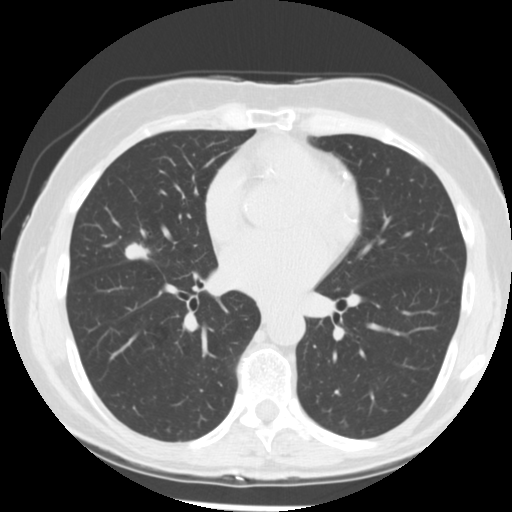
Chest CT (low-dose screening protocol), one axial image. First (baseline) screen. Lung window (W 1500 / L -600 HU). 2.5 mm slice thickness. Standard (soft-tissue) reconstruction kernel (STANDARD). Female participant, aged 66 years at enrolment. Former smoker at enrolment.
Lesion marked by an expert reader, box from (x=119, y=232) to (x=166, y=268) px. The exam's reader record, not a measurement of the box and not confirmed to be the same lesion: non-calcified nodule or mass ≥4 mm, right middle lobe, 15 × 13 mm, poorly defined margins, soft tissue attenuation. Lung cancer was diagnosed 27 days after this screen: adenocarcinoma, NOS, right middle lobe, undifferentiated (G4), stage IIIA (AJCC 6th edition), 18 mm at pathology.